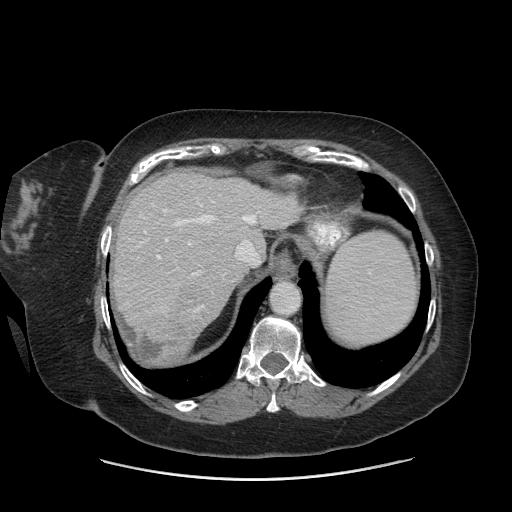
Contrast-enhanced abdominal CT (liver protocol), one axial slice. Slice 57 of 69 in the series (ordered by position). Reconstruction kernel STANDARD. 140 kVp. Soft-tissue window (W 400 / L 40 HU). 512 × 512 image matrix, field of view 420 × 420 mm. Case-level facts recorded for this patient, not image findings: diagnosis: hepatocellular carcinoma (patient treated with transarterial chemoembolisation; whether this scan precedes or follows treatment is not stated here); TNM stage (as recorded): Stage-IIIB.
Annotated regions visible in this slice (semi-automatic segmentation, software-assisted and operator-edited):
- abdominal aorta: bounding box [x1, y1, x2, y2] px = [270, 281, 299, 314]
- liver parenchyma outside the tumour (the mass and vessels are separate outlines, so this box may not span the whole liver): [112, 170, 302, 352]
- mass: [138, 310, 193, 361]
- liver vessels: [141, 204, 259, 311]